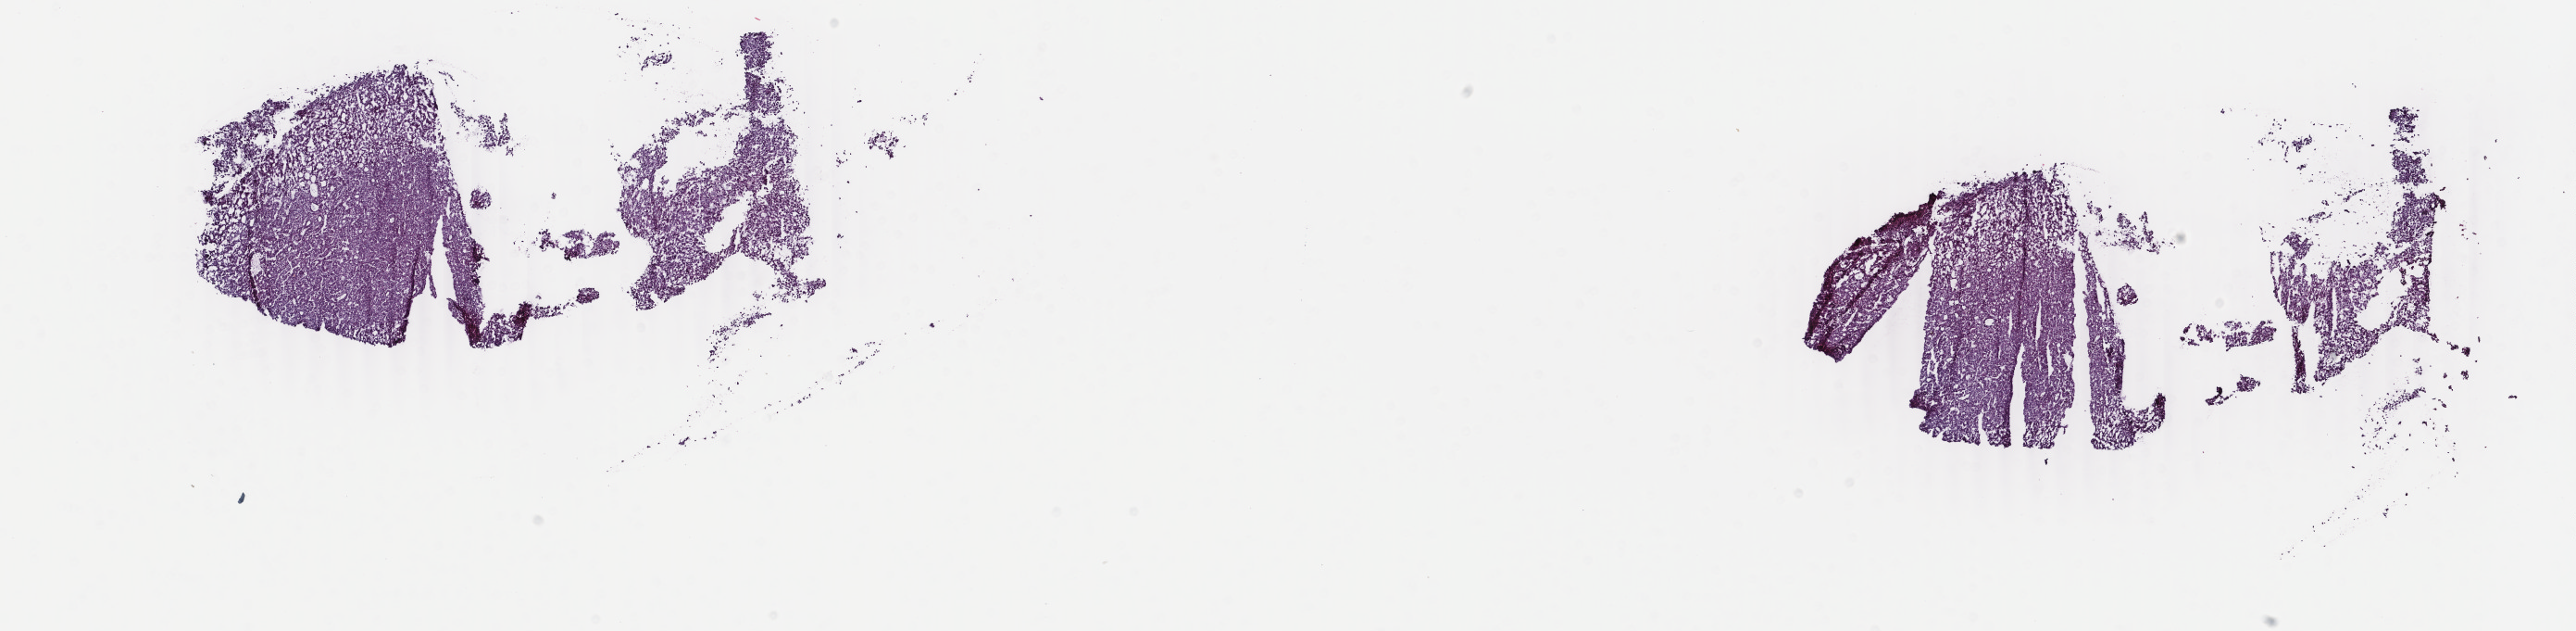
Whole-slide histology image, H&E-stained, shown as a low-resolution overview of the whole scanned area (about 22.1 x 5.4 mm). Frozen section from the top of the tissue portion. Primary tumour sample from the liver. Male patient; age at initial diagnosis 62 years.
Diagnosis: Hepatocellular carcinoma, NOS.